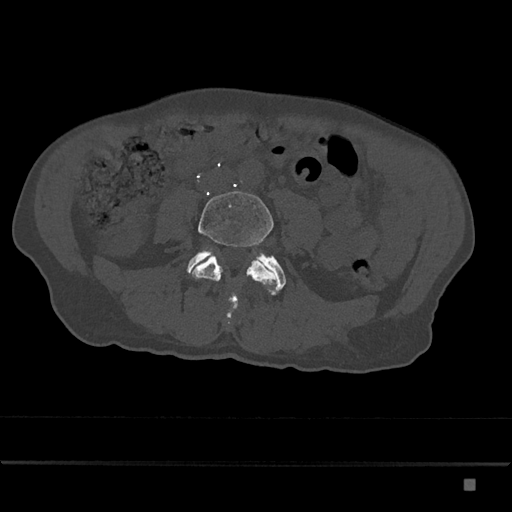
CT including the spine, one axial slice. Position 320 of 797 along the scan axis. Reconstruction kernel Br40s/3. 120 kVp. Bone window (W 1800 / L 400 HU). 0.5 mm slice thickness. 512 × 512 image matrix, field of view 390 × 390 mm. Patient: male, 72 years. Case-level facts recorded for this patient, not image findings: primary cancer: prostate.
Structures marked on this image (semi-automatically segmented with operator editing):
- L4 vertebra: bounding box [x1, y1, x2, y2] px = [190, 191, 277, 311]
- L5 vertebra: [187, 248, 286, 318]